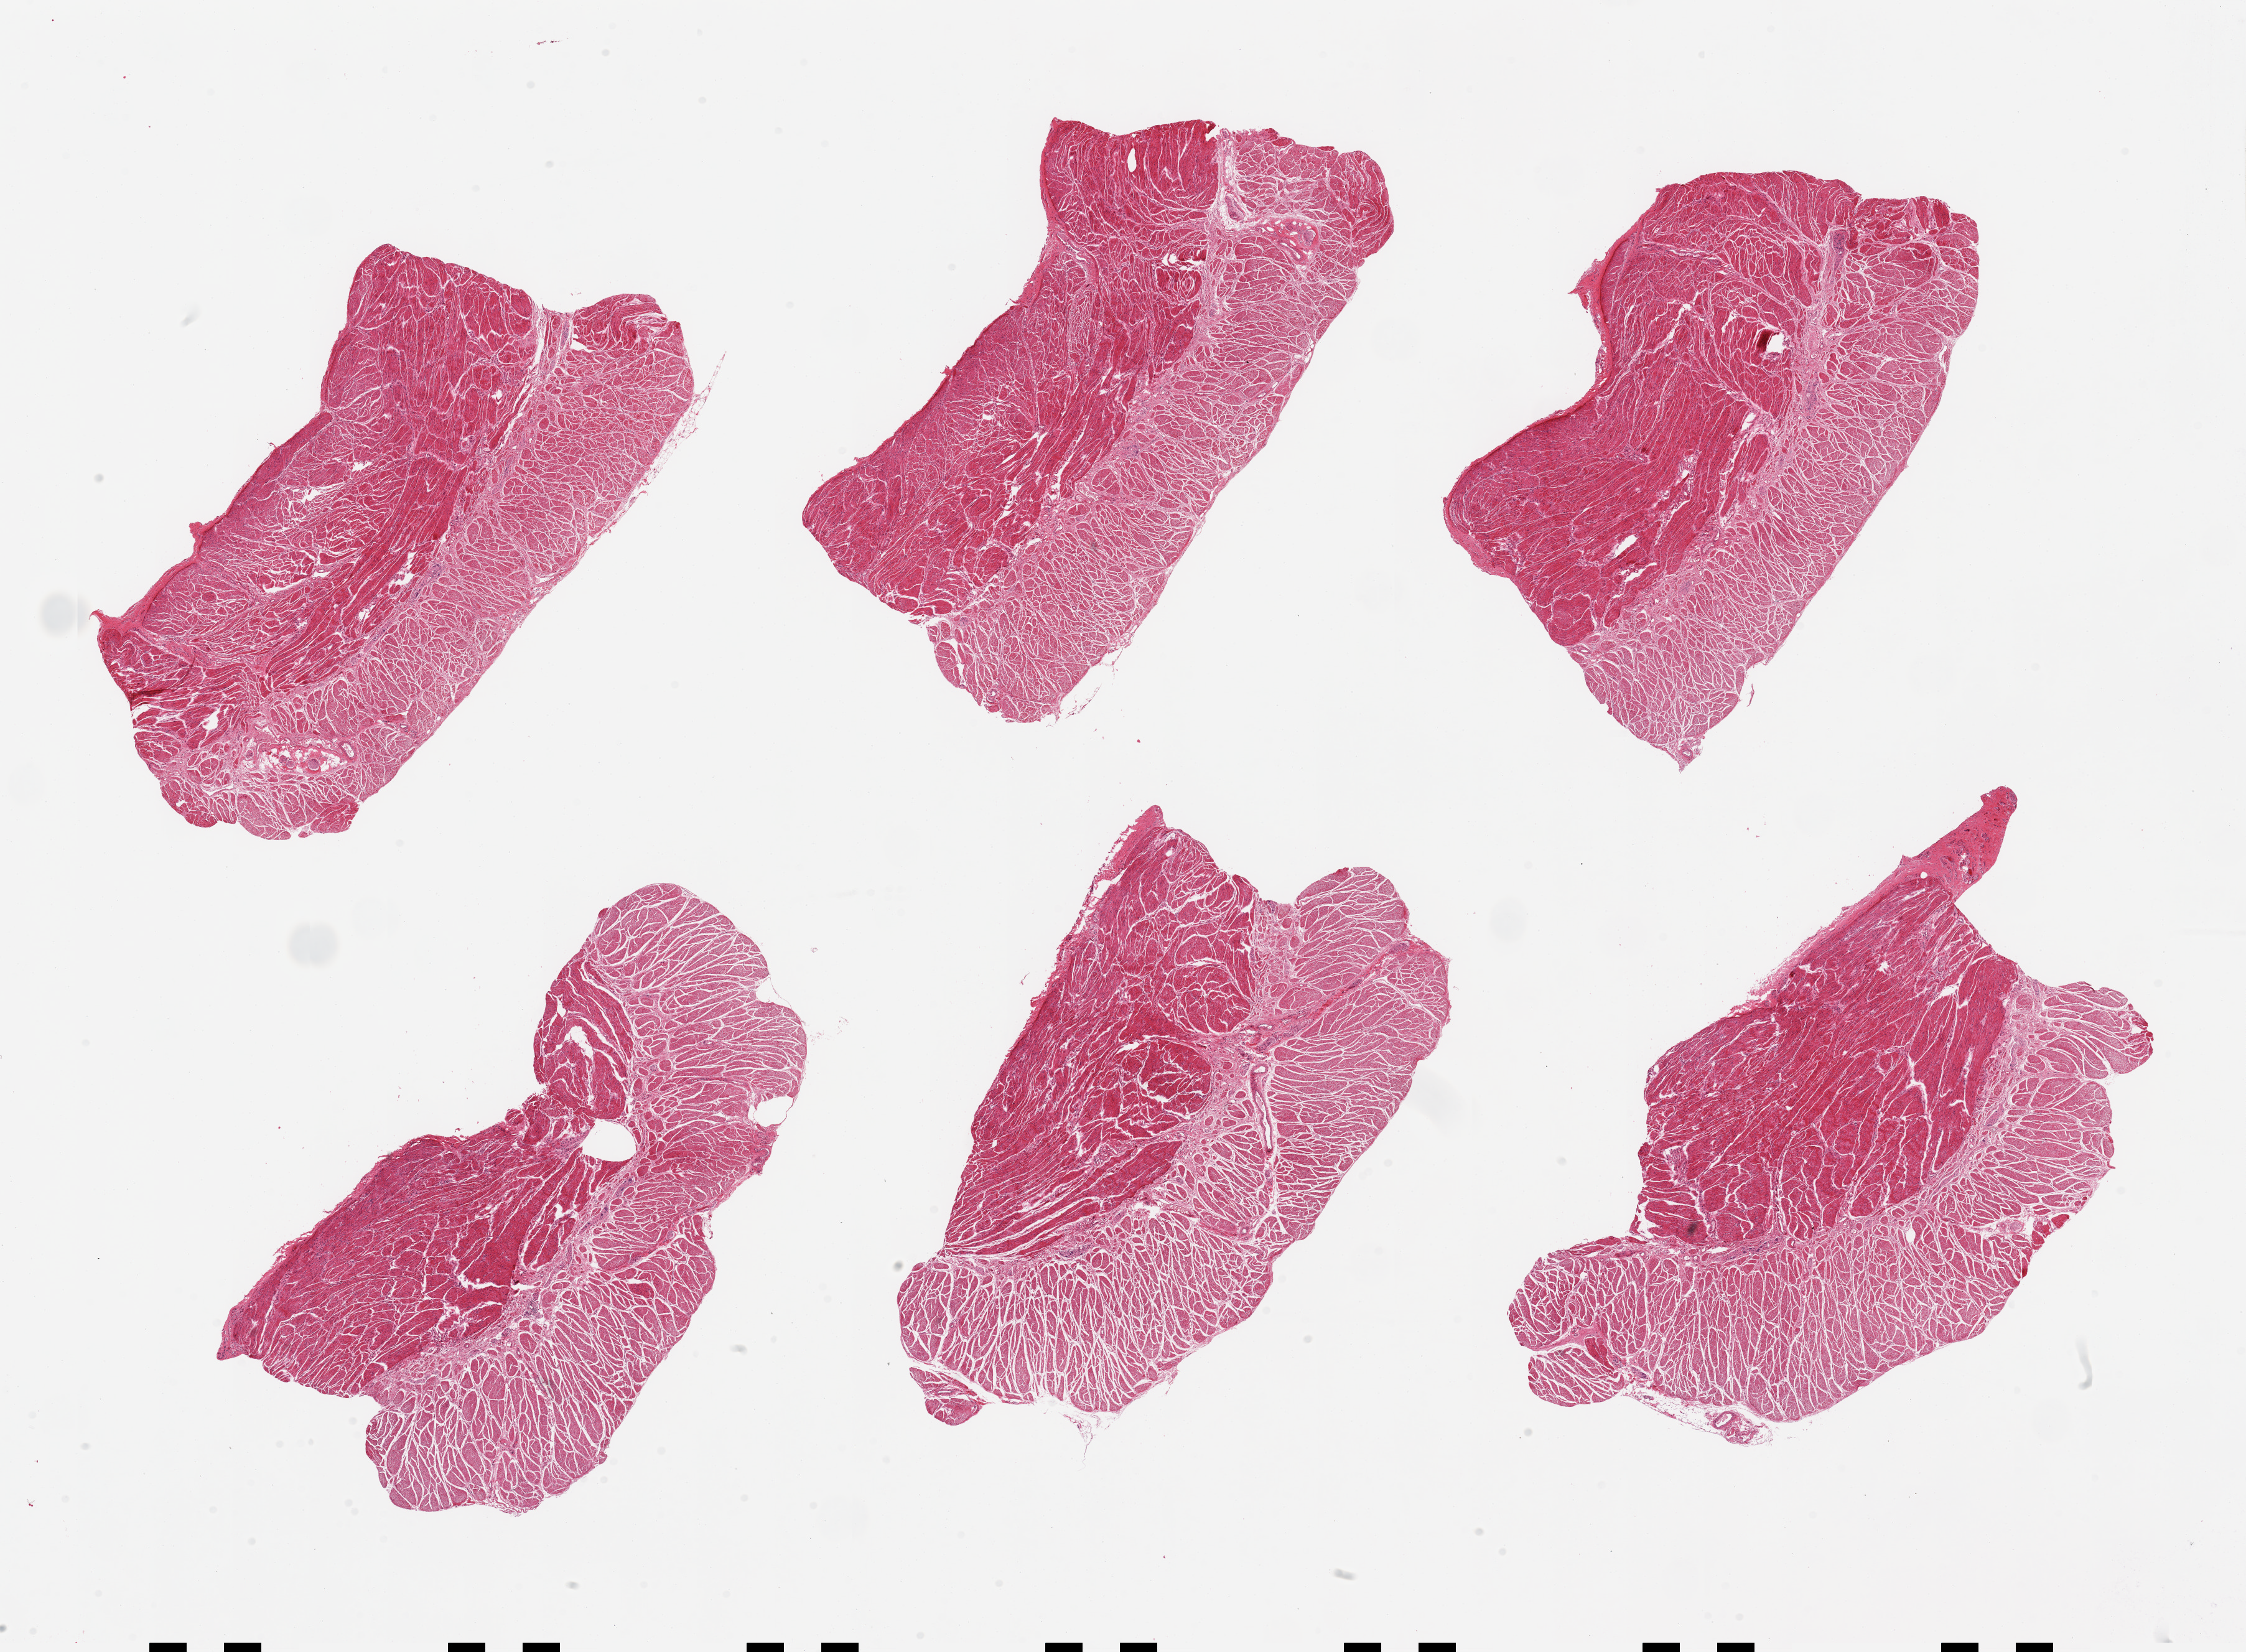
Whole-slide image, H&E stain — low-resolution overview of the scanned area, about 28.5 x 21.0 mm, PAXgene-fixed paraffin-embedded (PFPE) section, target tissue: gastroesophageal junction, tissue donor sample.
Review note (as recorded): 6 pieces; well trimmed.